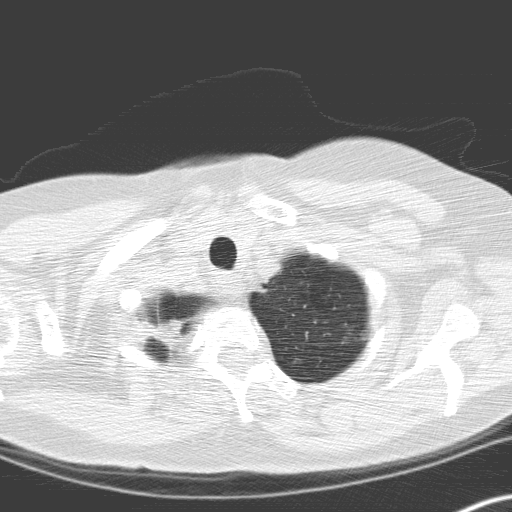
Low-dose screening chest CT, axial slice, second annual screen, lung window (W 1500 / L -600 HU), 3.2 mm slice thickness, 120 kVp, slice 21 of 166 in the series, 512 × 512 image matrix. Female, age 60 years at enrolment.
Expert reader's lesion annotation, bounding box [x1, y1, x2, y2] px = [125, 308, 195, 369]. The exam's reader record, not a measurement of the box and not confirmed to be the same lesion: non-calcified nodule or mass ≥4 mm, right upper lobe, 12 × 8 mm, spiculated (stellate) margins, soft tissue attenuation, pre-existing on the prior screen: no.